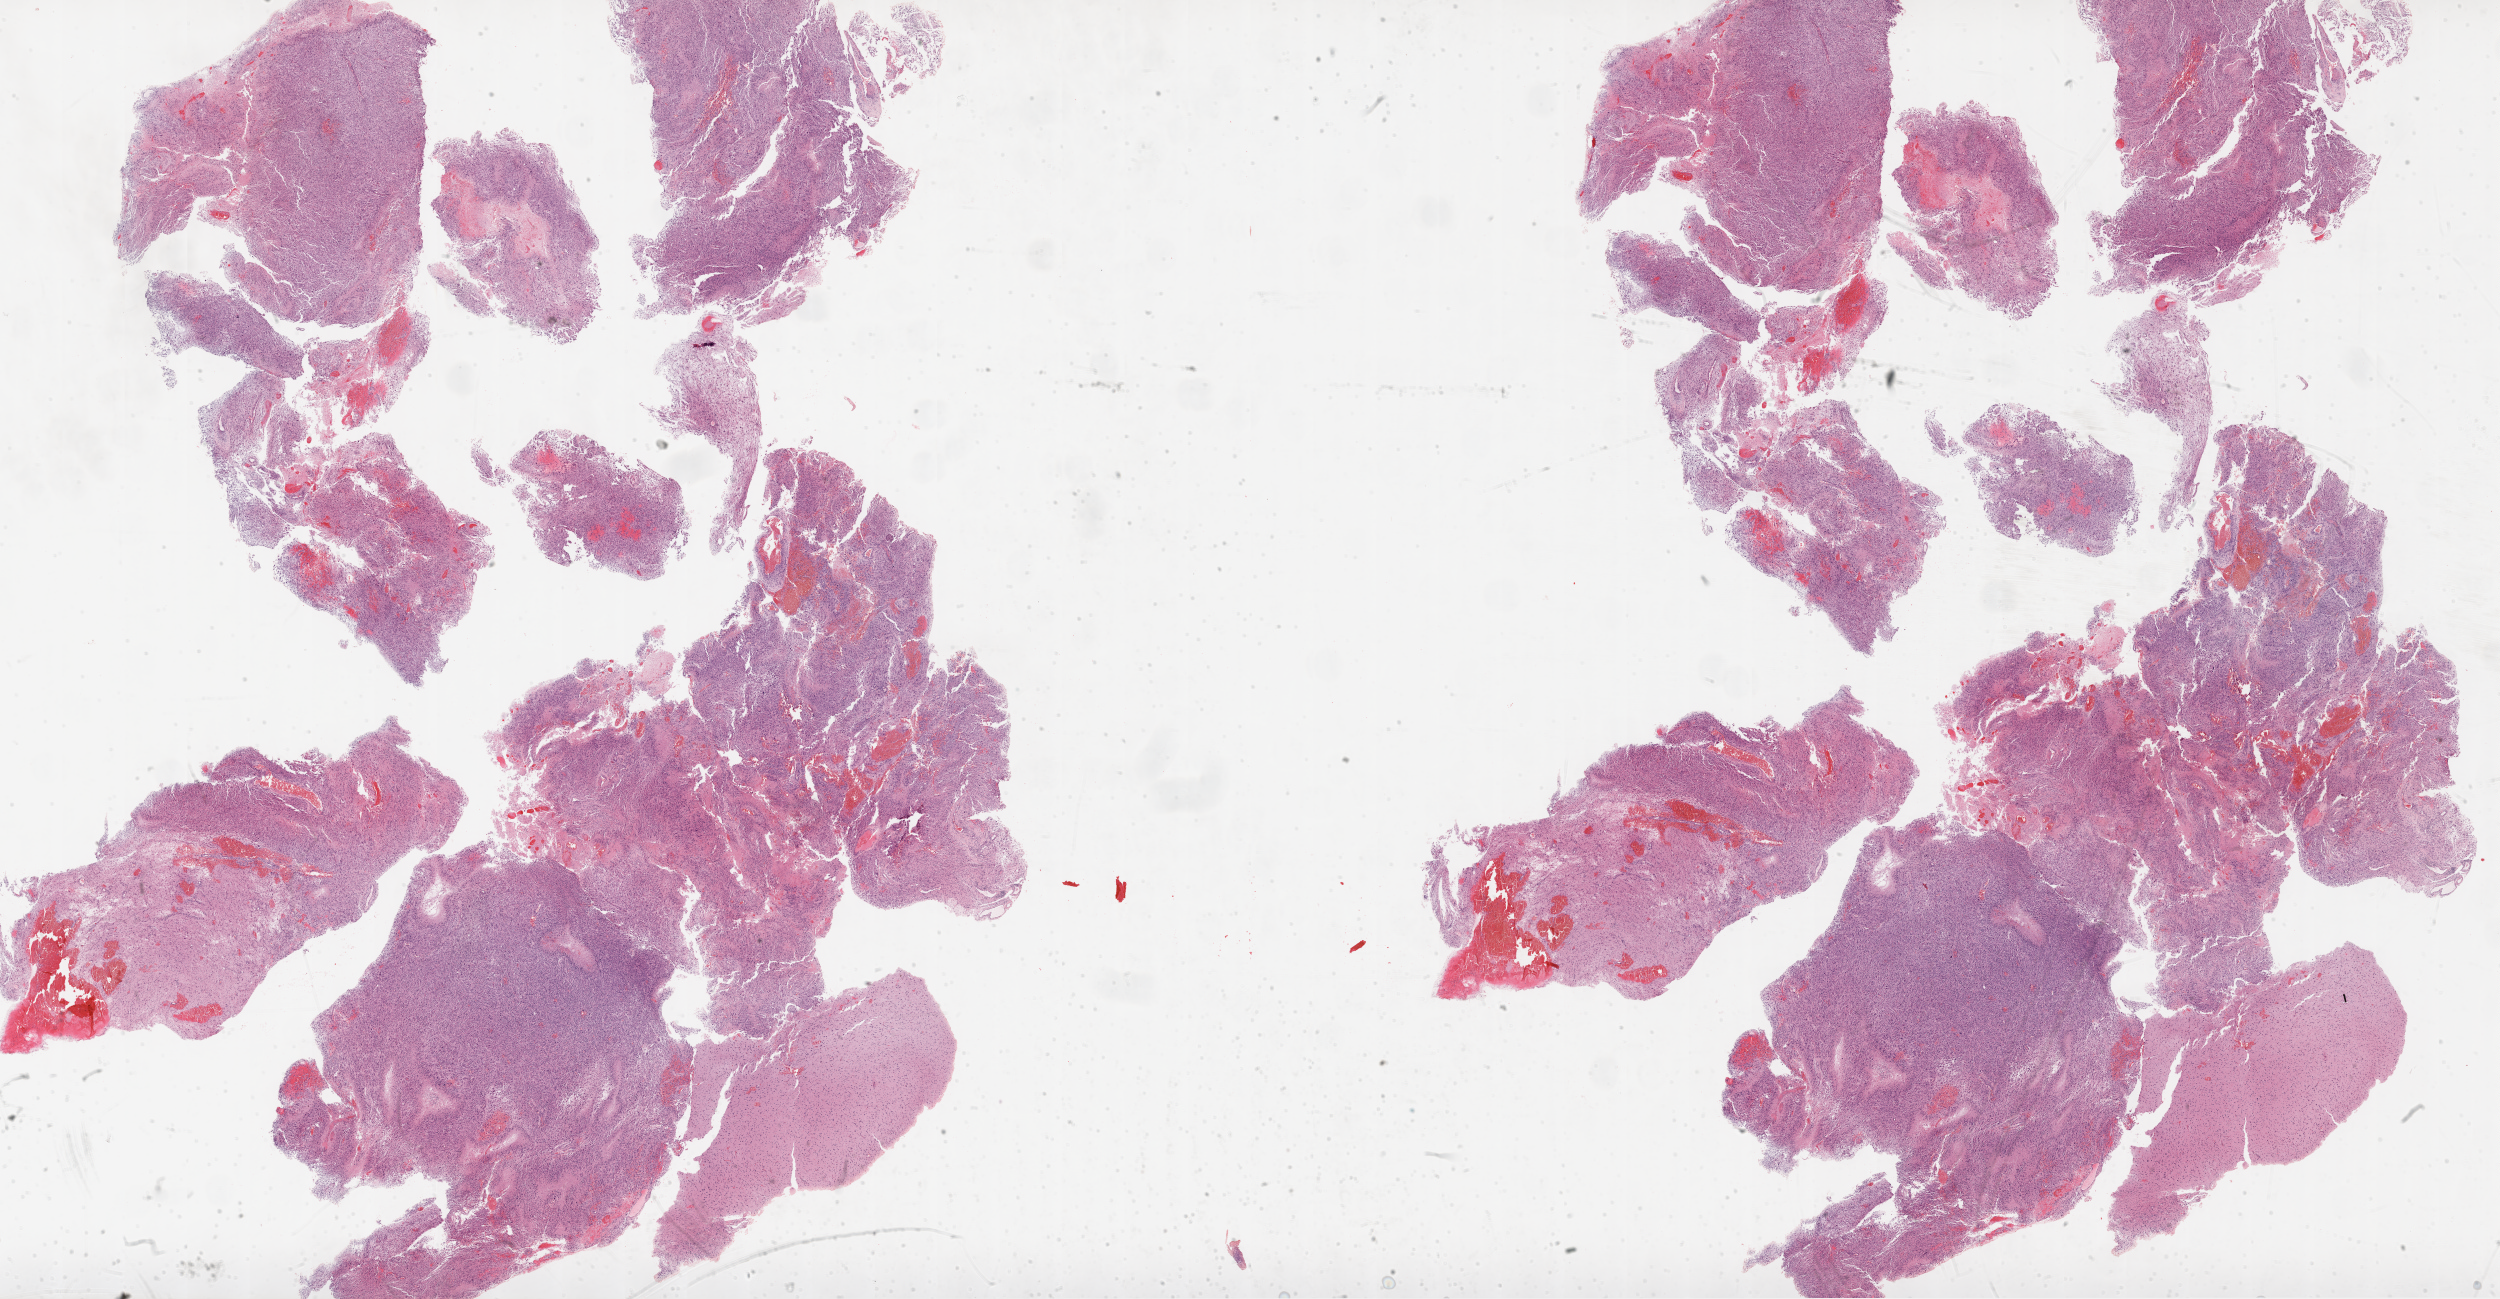
Whole-slide histology image, H&E-stained, shown as a low-resolution overview of the whole scanned area (about 40.1 x 20.8 mm); formalin-fixed paraffin-embedded (FFPE) diagnostic section; brain, primary tumour sample. Patient: female, age at initial diagnosis 78 years.
- pathologic diagnosis: Glioblastoma